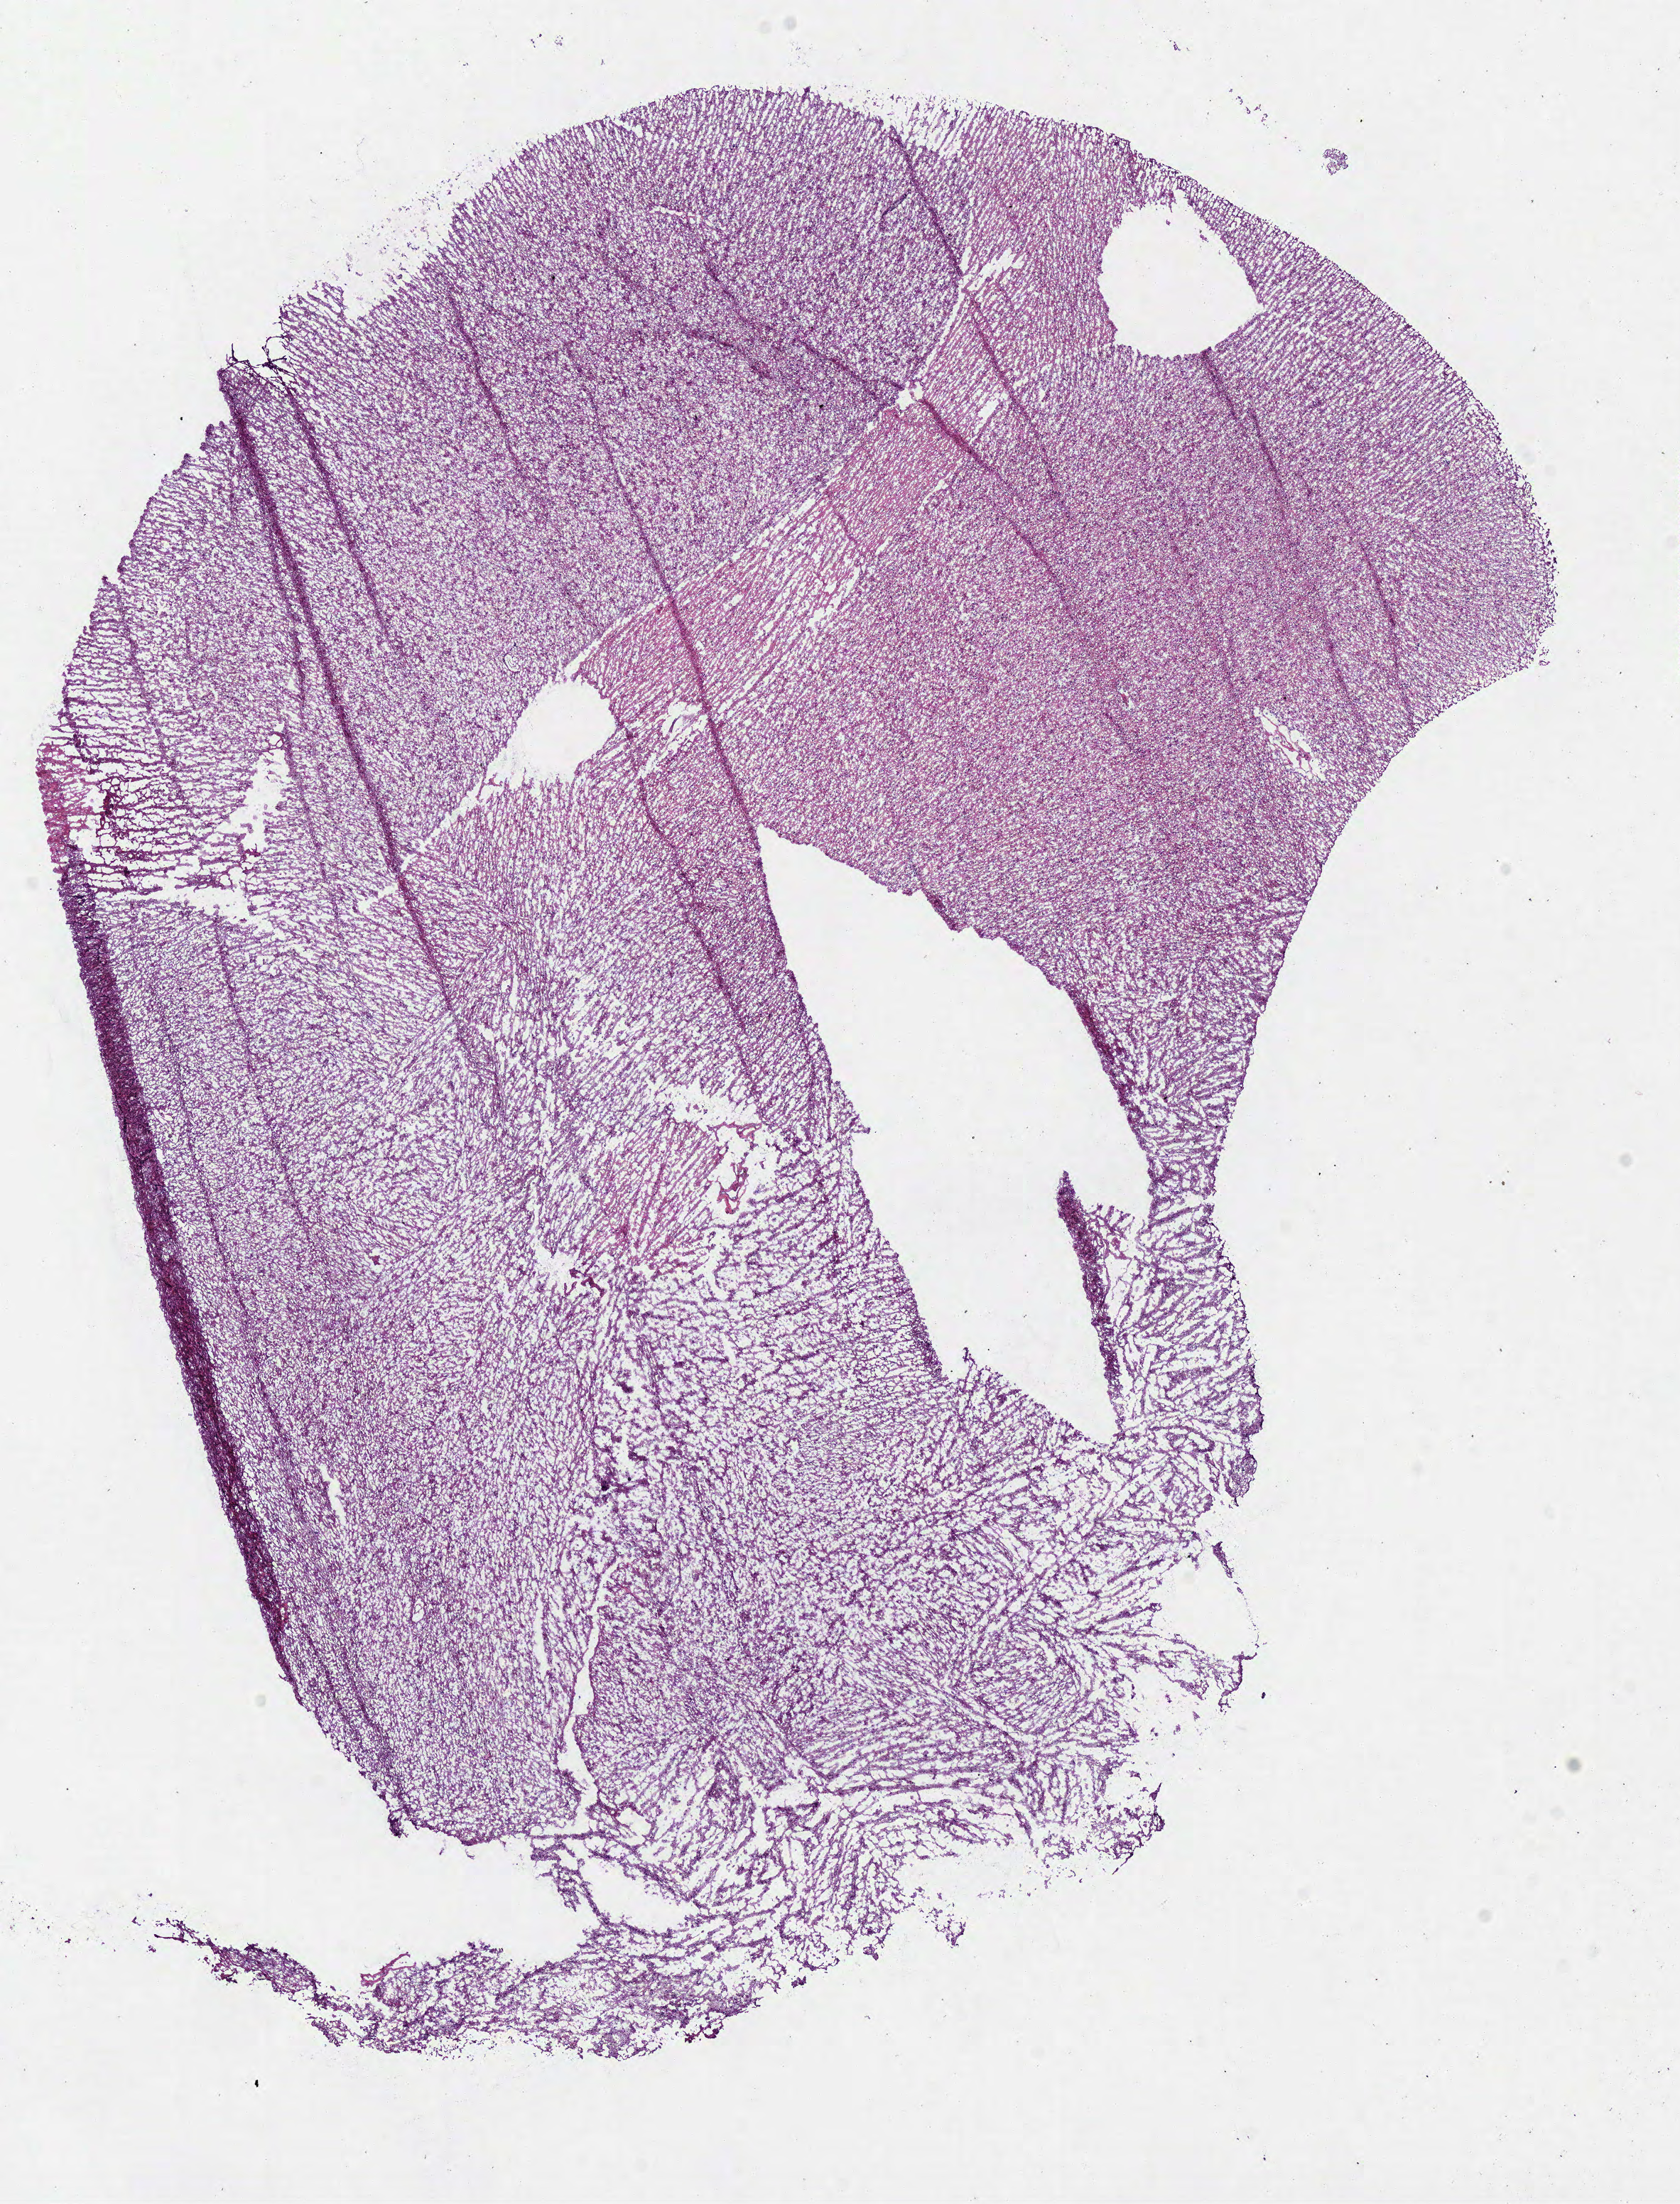
H&E whole-slide image, shown as a low-resolution overview of the whole scanned area (about 9.3 x 12.2 mm), frozen section from the bottom of the tissue portion, sample: primary tumour, brain. Female, age 60 years at initial diagnosis. Histologic grade: G3 (poorly differentiated). Composition of this section per pathologist review: tumour cells 100%, tumour nuclei 75%, normal cells 0%, stromal cells 0%, necrosis 0%.
Diagnosis: Mixed glioma.